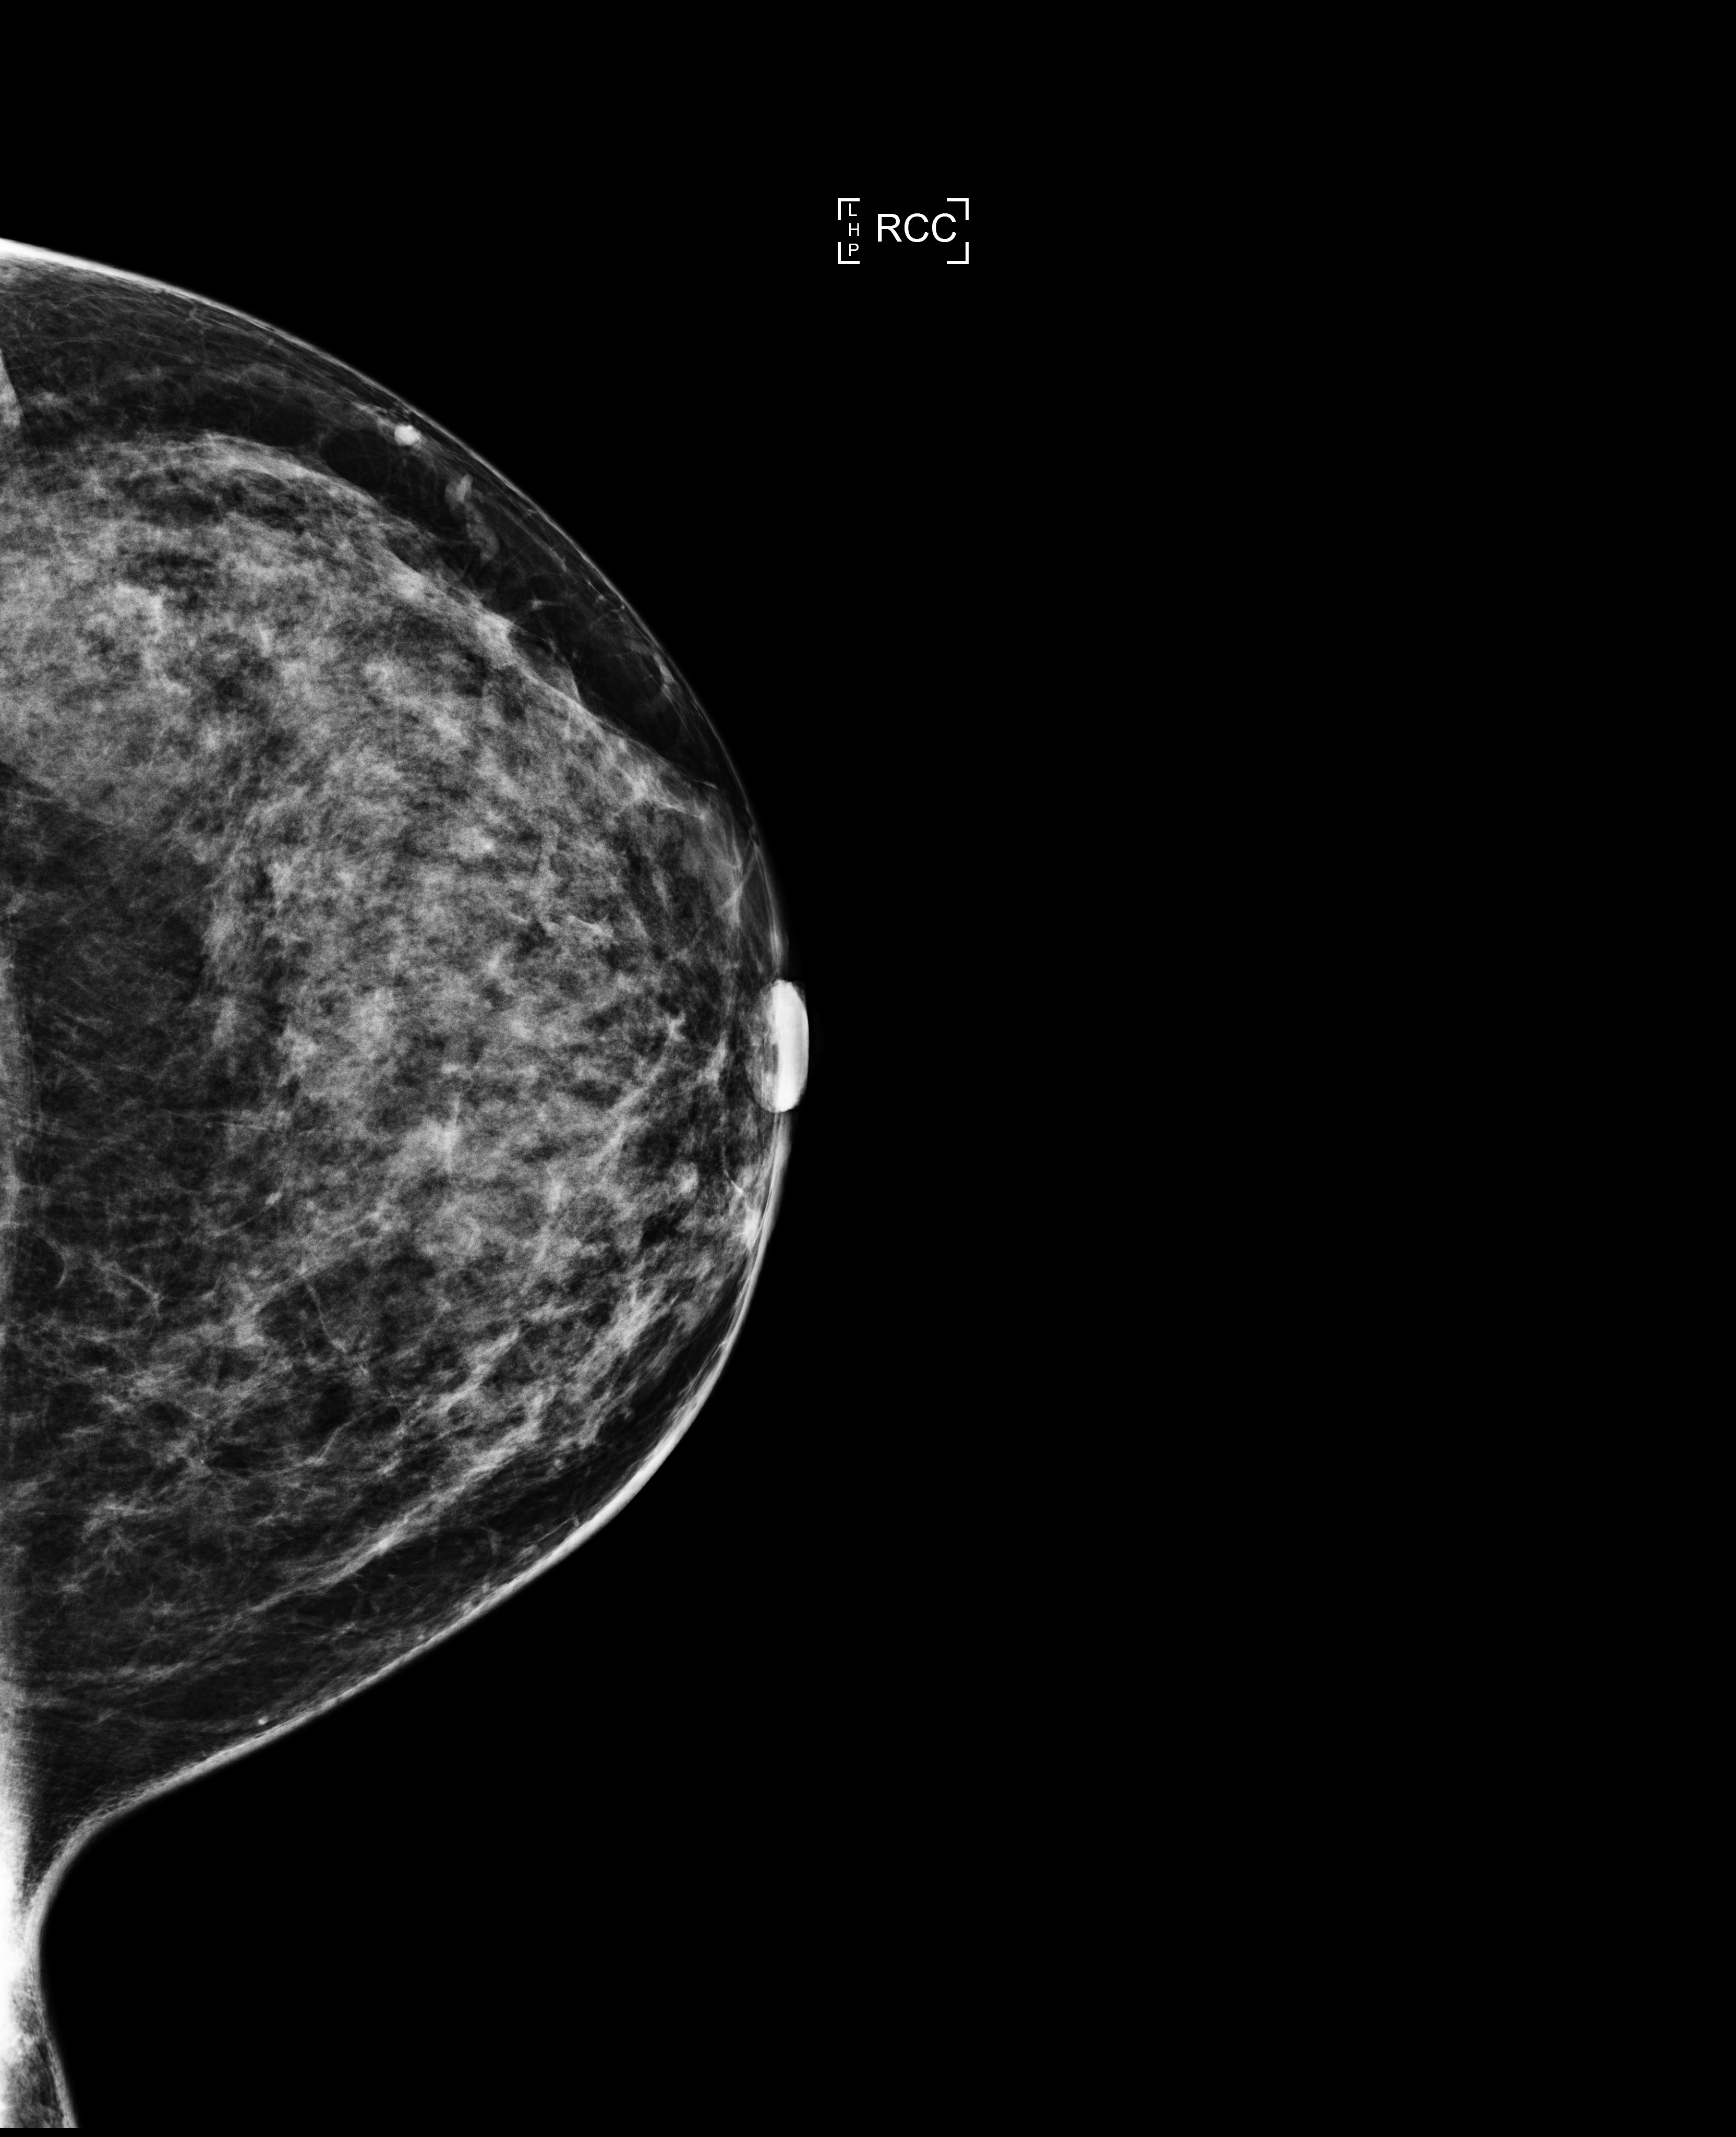
Digital mammogram (FFDM); right breast; CC view; screening examination; compressed breast thickness 71 mm. Female patient, age 42 years.
BI-RADS breast density category at the screening exam (both breasts, scale 1–4): 3. Final BI-RADS category for the screening round (tomosynthesis exam, both breasts): category 1. Recall: no recall after this screen.